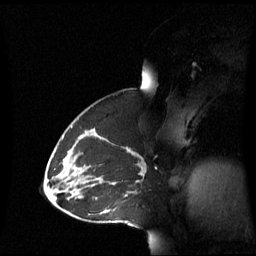
Breast MRI (dynamic contrast-enhanced), one sagittal slice; position 37 of 60 along the scan axis; dynamic contrast-enhanced series, image 2 of 3 at this slice position (ordered by acquisition); 1.5 T; TE 4.2 ms, TR 8.4 ms; 2.8 mm slice thickness; 256 × 256 image matrix, field of view 270 × 270 mm. Patient: female, 43 years. From the clinical record (not read from this slice): setting: breast cancer imaged before/during neoadjuvant chemotherapy; receptor status: triple-negative.
Annotated regions visible in this slice (semi-automatically segmented with operator editing):
- analysis volume of interest (the breast-tissue region the enhancement analysis was run in; not a lesion): box from (x=69, y=137) to (x=143, y=198) px
- tumour enhancement mask (voxels above the 70 % enhancement threshold inside the analysis volume of interest): (x=125, y=147)–(x=143, y=197)